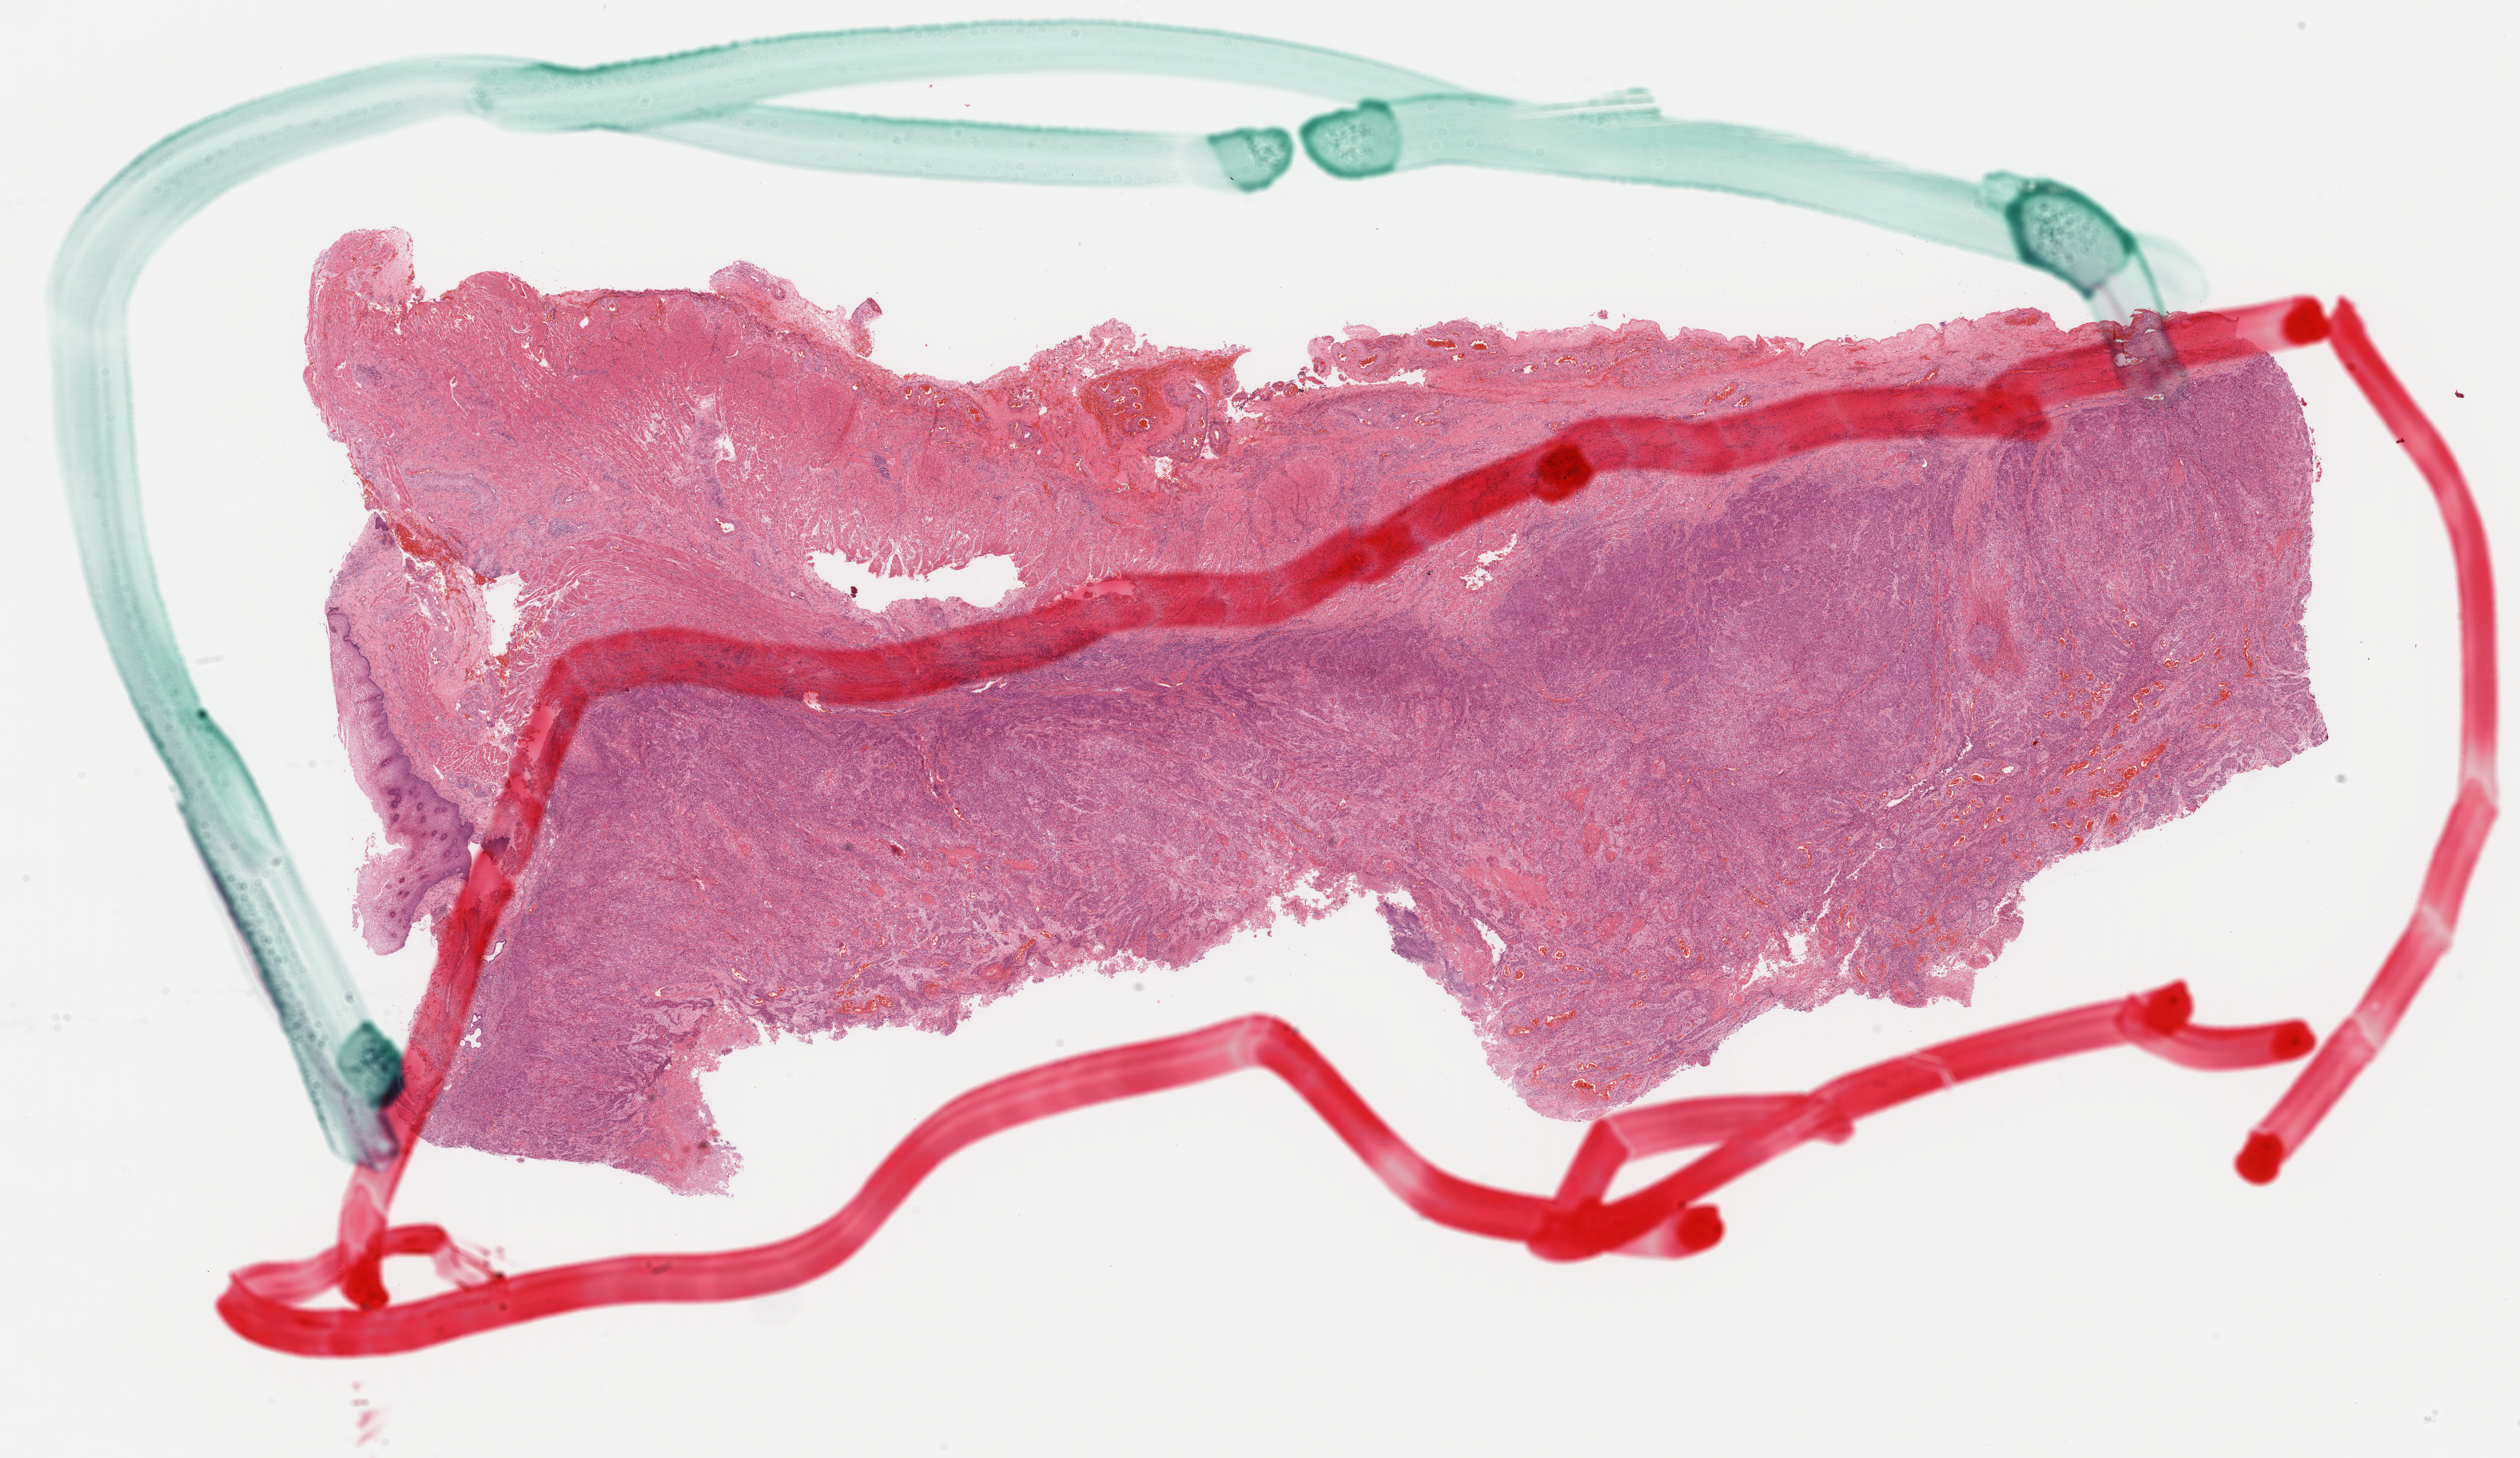
Whole-slide histology image, Hematoxylin and eosin (H&E) stained — whole scanned area (about 24.9 x 14.4 mm, from a 40x scan) shown as a low-resolution overview. Formalin-fixed paraffin-embedded (FFPE) diagnostic section. Sample: primary tumour, esophagus. Male, age 54 years at initial diagnosis. Histologic grade: G1 (well differentiated).
AJCC pathologic stage: IIB (7th edition). Pathologic diagnosis: Squamous cell carcinoma, keratinizing, NOS (lower third of esophagus). Lymph nodes positive (case pathology): 2 of 10 examined.